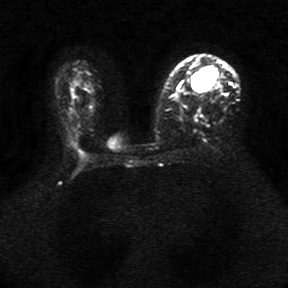
Breast MRI, one axial slice; slice 20 of 34 in the series (ordered by position); diffusion-weighted series; image 2 of 4 stored at this slice position (different b-values; order by instance number); 1.5 T; 5 mm slice thickness; 288 × 288 image matrix, field of view 340 × 340 mm. Female patient.
Structures marked on this image (expert manual segmentation):
- tumour on diffusion-weighted imaging: bounding box [x1, y1, x2, y2] px = [193, 68, 210, 91]